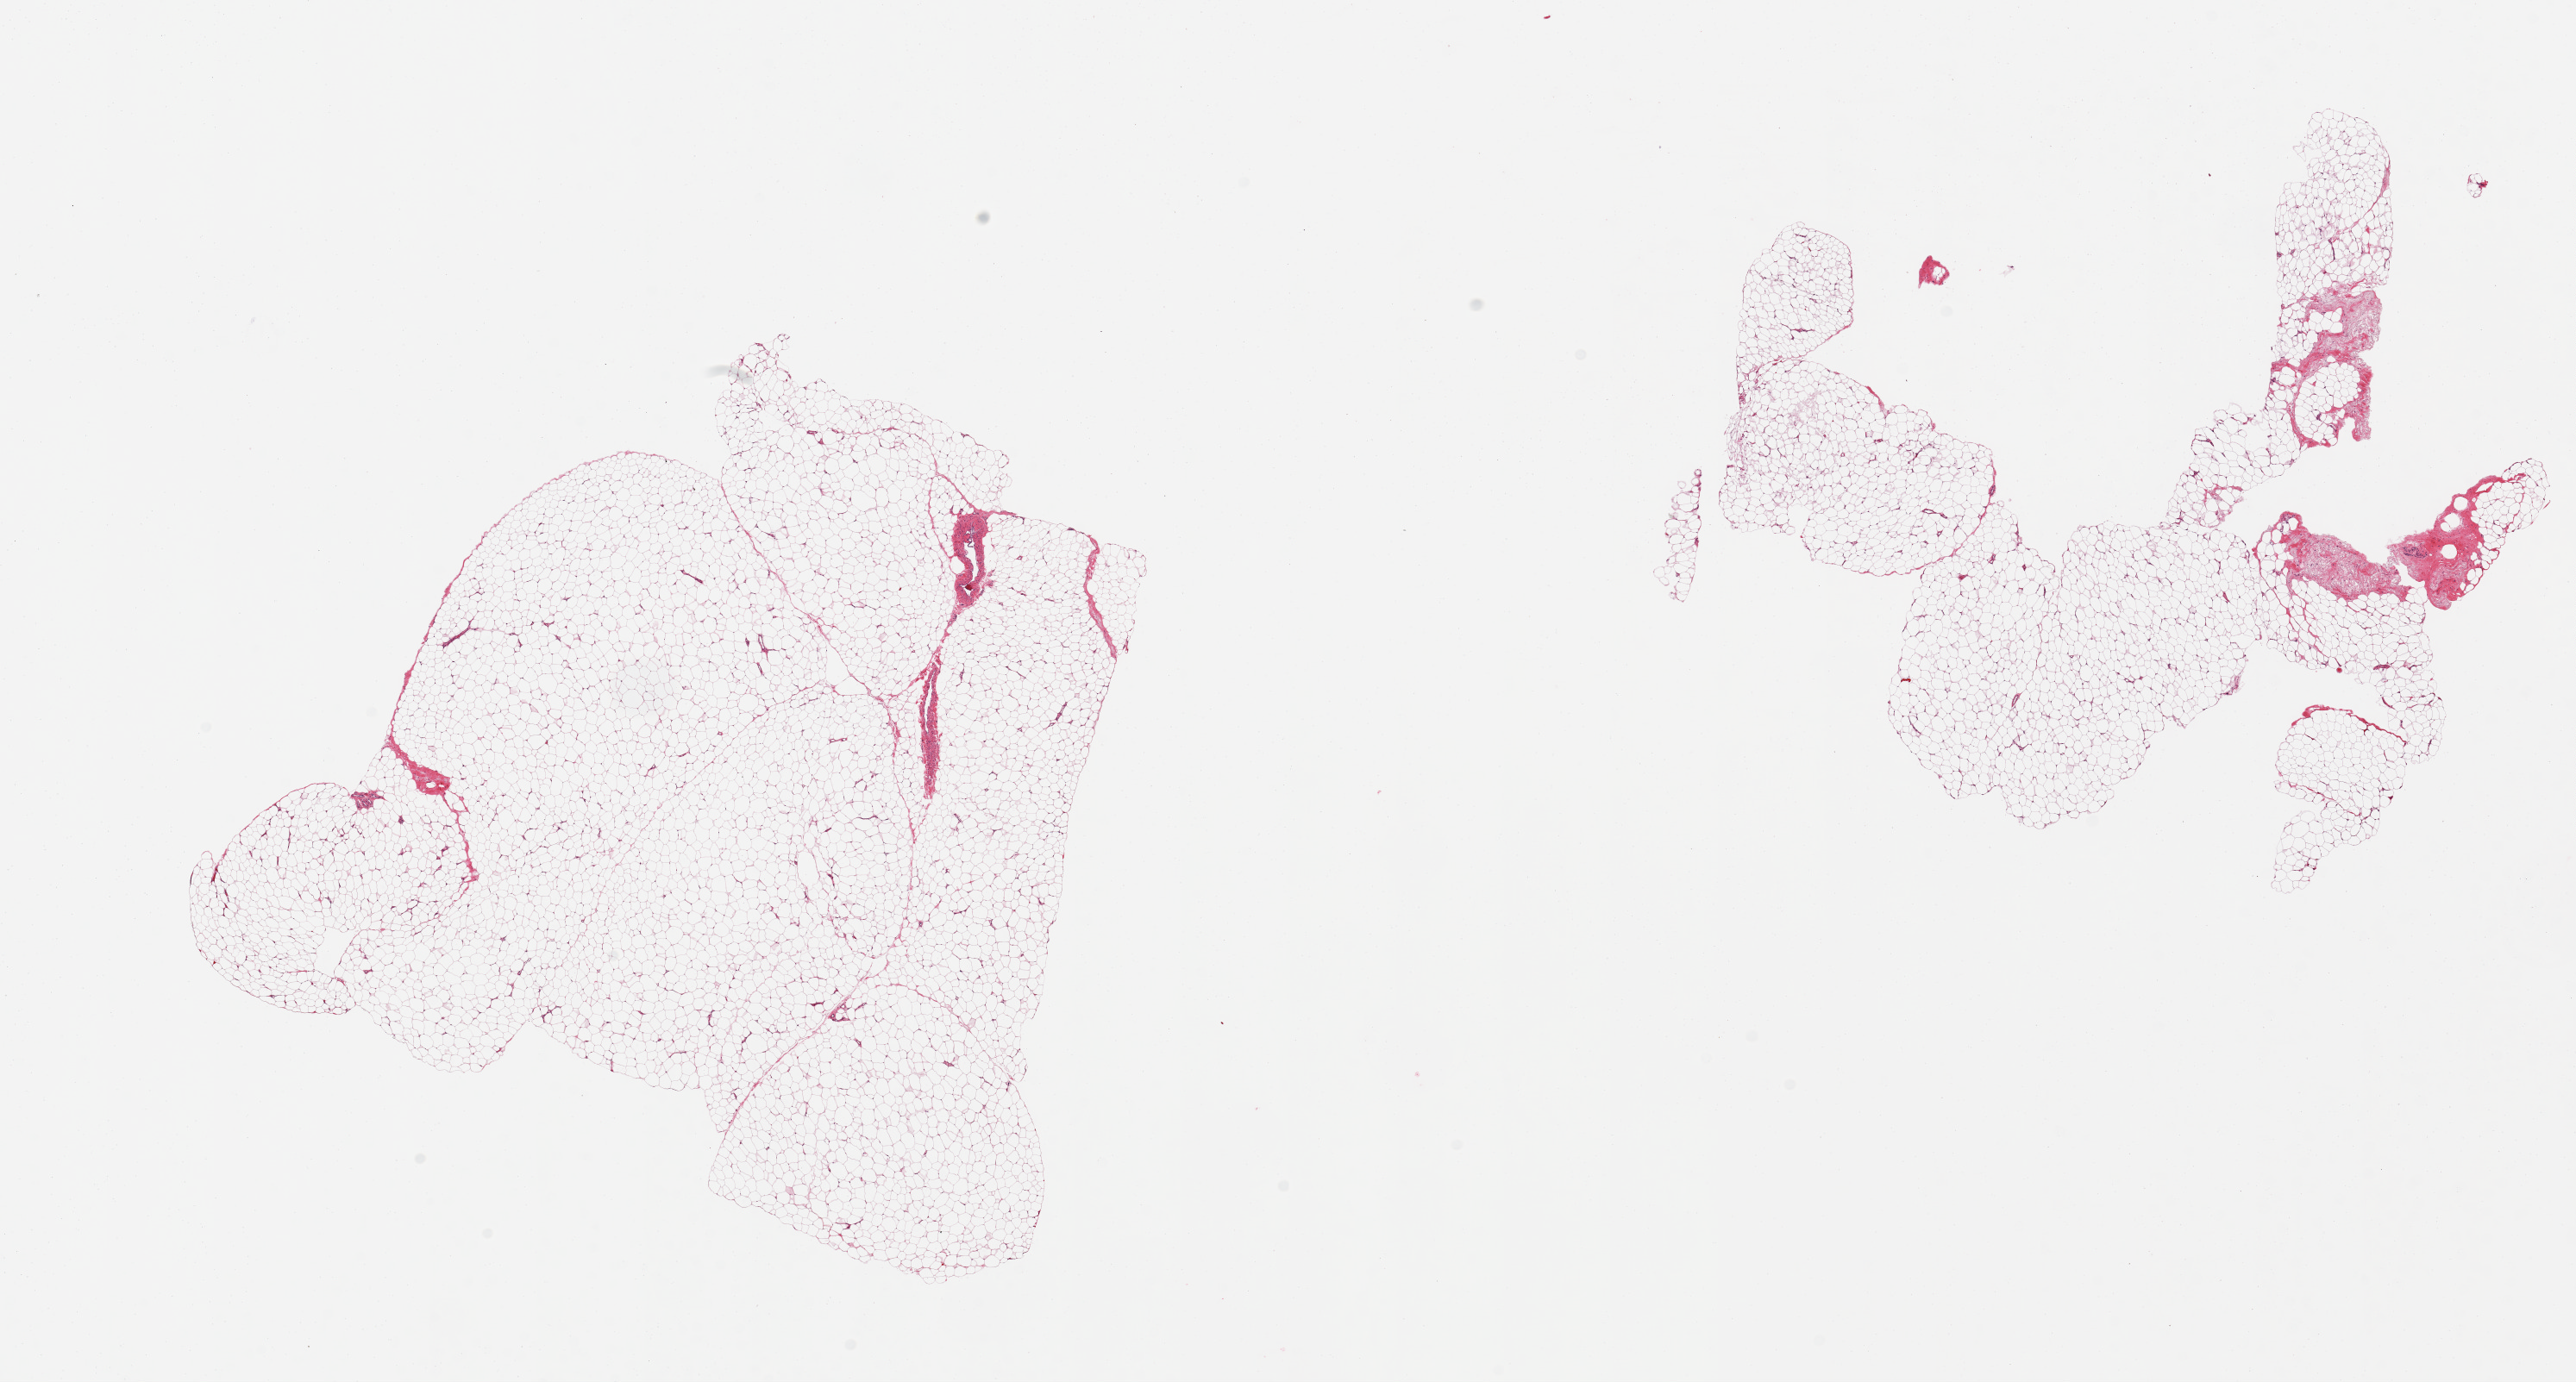
Whole-slide image, H&E stain, shown as a low-resolution overview of the whole scanned area (about 23.6 x 12.7 mm, slide scanned at 20x); PAXgene-fixed, paraffin-embedded tissue; target tissue: adipose tissue; tissue donor sample. Male donor.
Reviewer comment on this tissue sample: 2 pieces, <5% fascia.